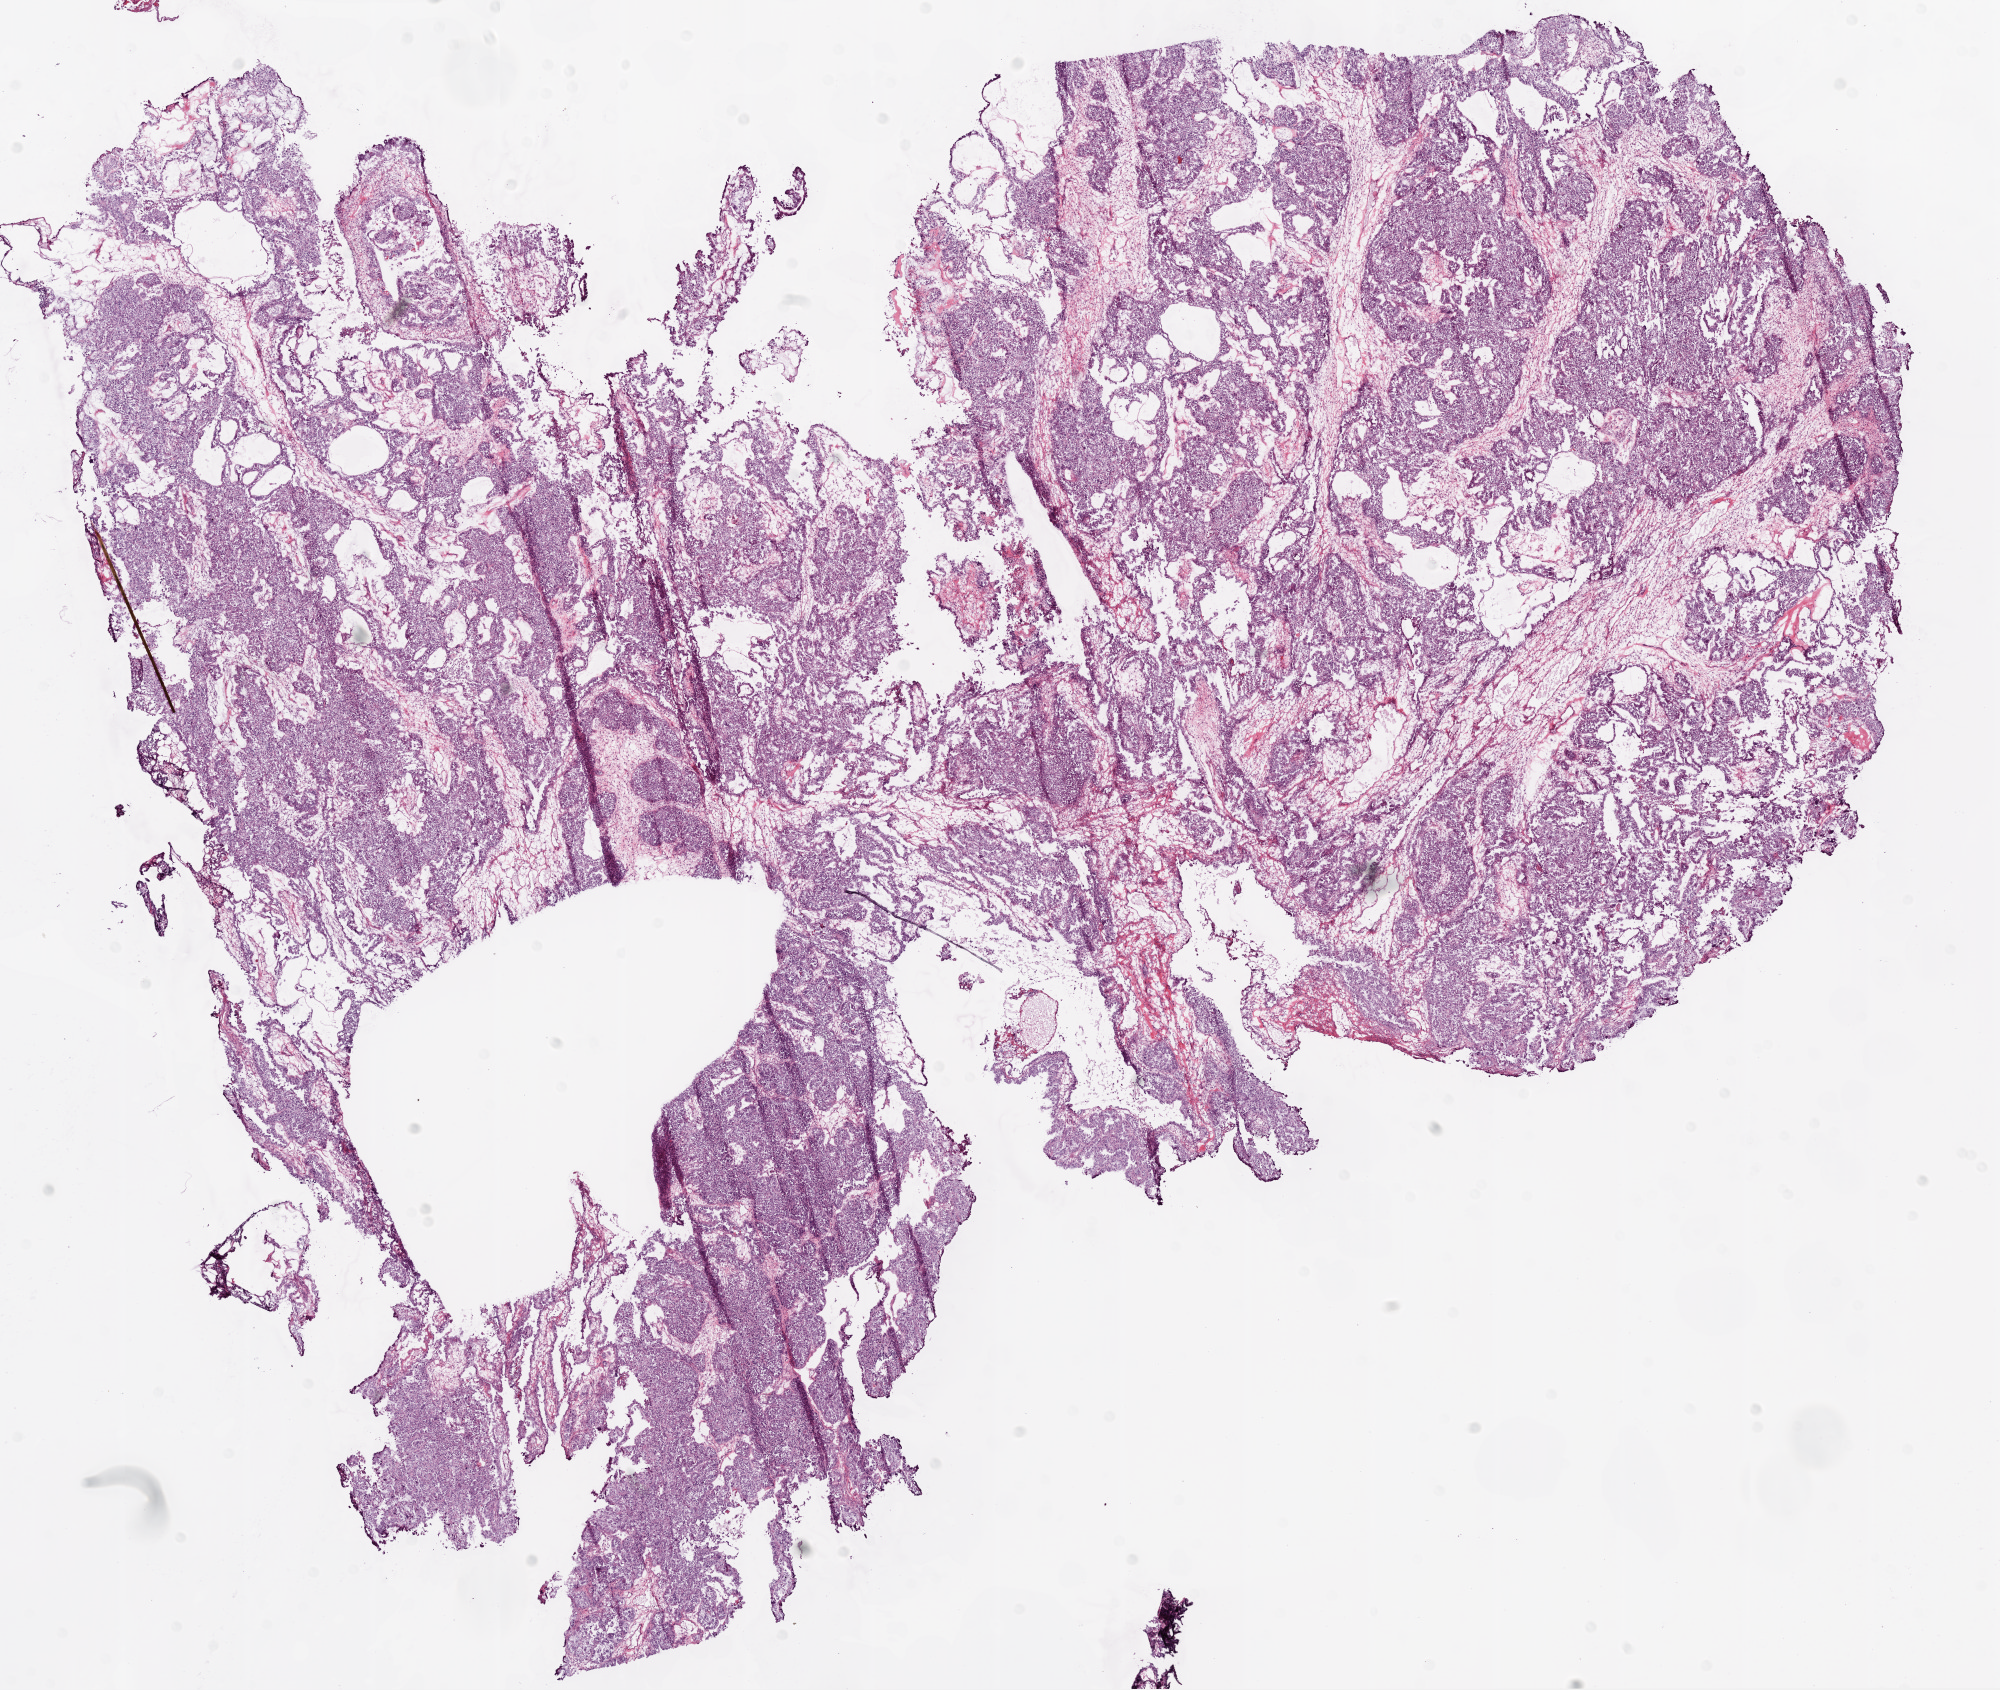
Digitized H&E-stained tissue section (whole slide), a low-resolution overview of the entire scanned area, about 16.0 x 13.6 mm (from a 20x scan). Frozen section. Ovary, primary tumour sample. Female patient; age at initial diagnosis 43 years. Histologic grade: G2 (moderately differentiated). Composition of this section per pathologist review: tumour cells 95%, tumour nuclei 70%, normal cells 0%, stromal cells 0%, necrosis 5%.
- histologic diagnosis: Serous cystadenocarcinoma, NOS
- laterality: bilateral
- FIGO stage: IIC